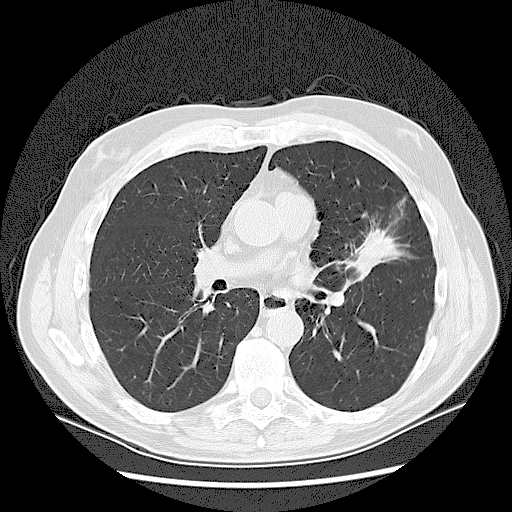
Axial slice from a low-dose chest CT screening exam. Baseline screening round. Lung window (W 1500 / L -600 HU). 2.5 mm slice thickness. 120 kVp. Male participant, aged 65 years at enrolment. Current smoker at enrolment.
- Expert-annotated lung lesion, box from (x=347, y=220) to (x=399, y=267) px.
- Reader record for this screening exam (exam-level; its link to the box is not recorded): non-calcified nodule or mass ≥4 mm, left upper lobe, 37 × 27 mm, spiculated (stellate) margins, soft tissue attenuation.
- Later outcome: lung cancer diagnosed 56 days after this screen — non-small cell carcinoma, poorly differentiated (G3), stage IA (AJCC 6th edition).